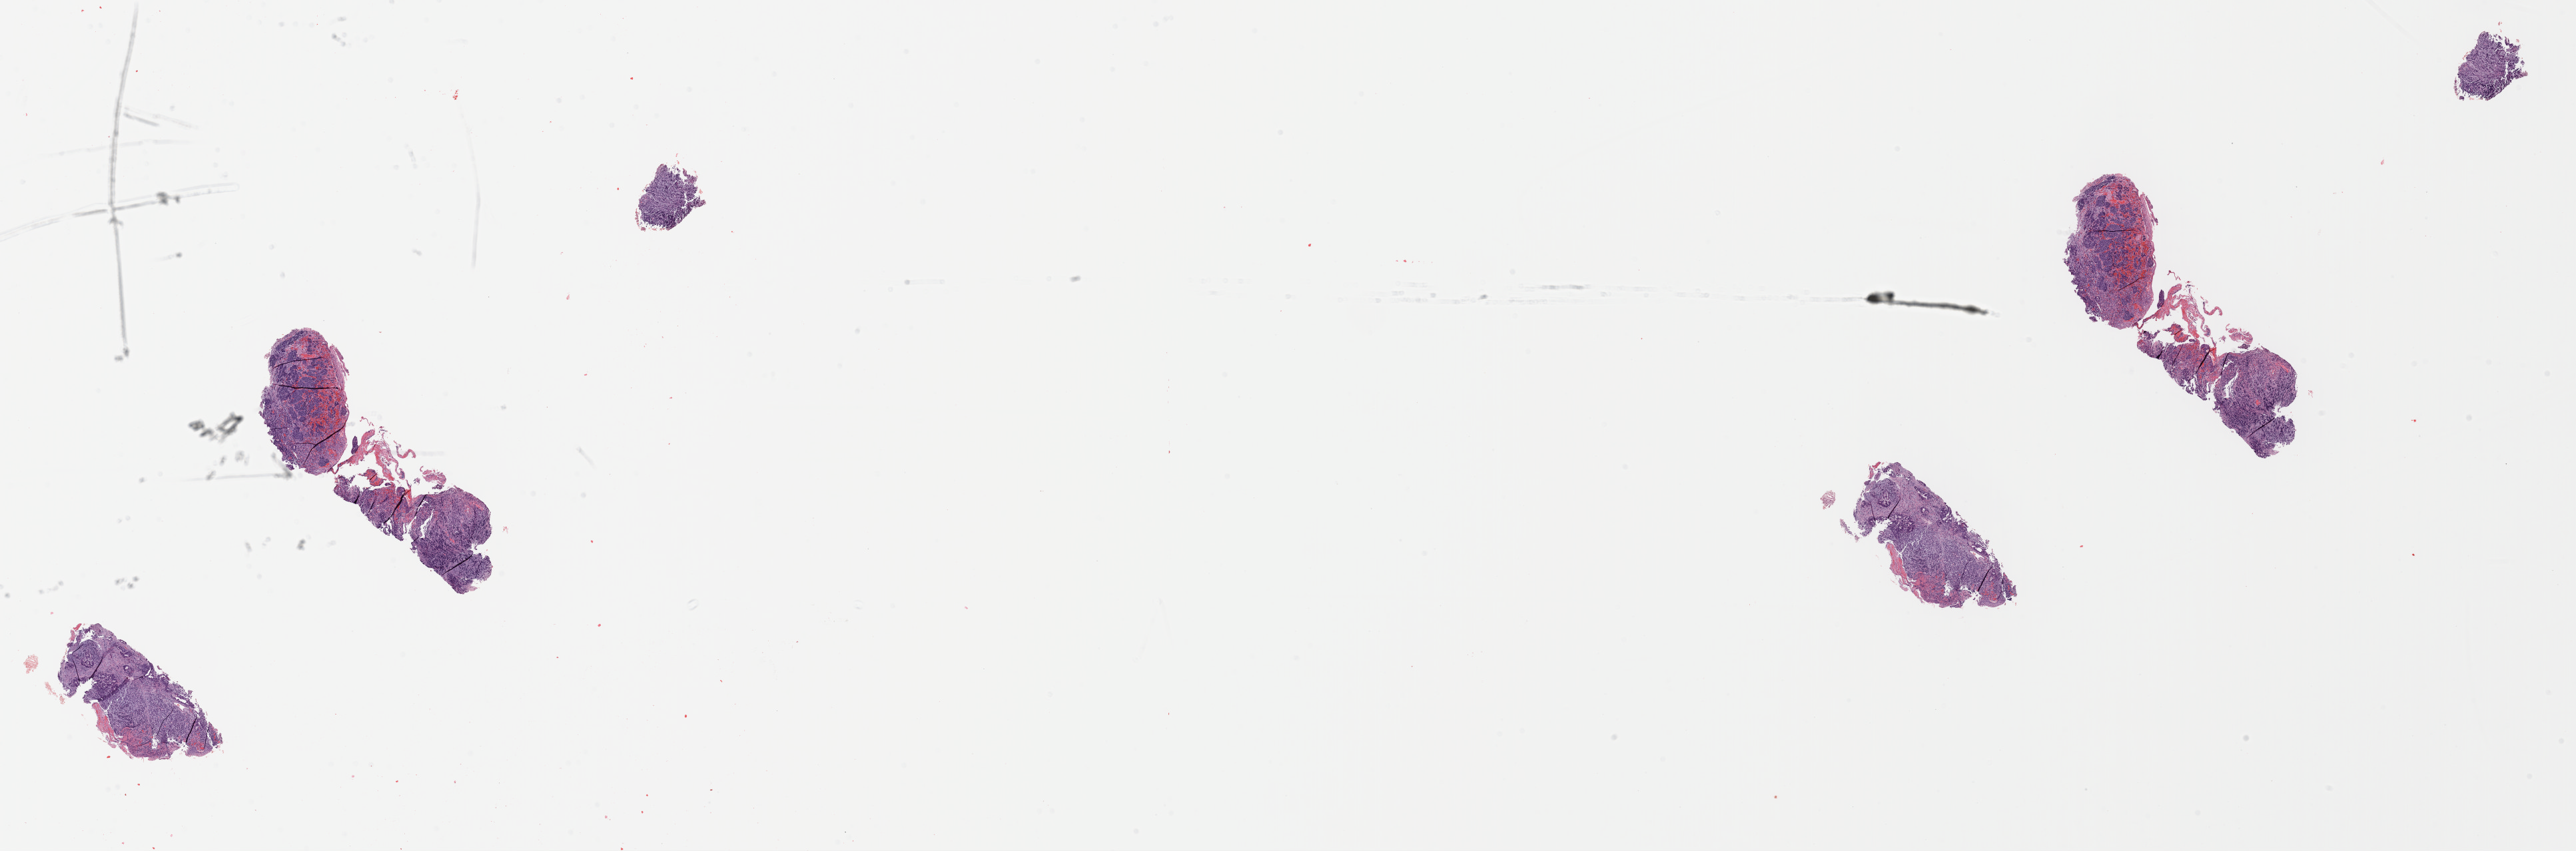
H&E-stained whole-slide image — whole scanned area (about 30.5 x 10.1 mm) shown as a low-resolution overview; formalin-fixed paraffin-embedded (FFPE) diagnostic section; esophagus, primary tumour sample. Male patient; age at initial diagnosis 58 years. Histologic grade: G3 (poorly differentiated). Pathologist review of this section (percent, as recorded): tumour cells 65%, tumour nuclei 95%, normal cells 2%, stromal cells 33%, necrosis 0%. Inflammatory infiltration, as recorded: lymphocyte infiltration 4%, monocyte infiltration 2%, neutrophil infiltration 4%.
- pathologic diagnosis: Adenocarcinoma, NOS (lower third of esophagus)